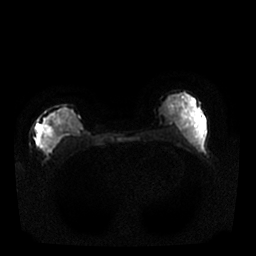
Breast MRI, one axial slice. Slice 13 of 25 in the series (ordered by position). Diffusion-weighted series; image 2 of 4 stored at this slice position (different b-values; order by instance number). 1.5 T. 4 mm slice thickness. 256 × 256 image matrix, field of view 340 × 340 mm. Female patient.
Annotated regions visible in this slice (outlined manually by an expert reader):
- tumour on diffusion-weighted imaging: box from (x=36, y=125) to (x=52, y=150) px